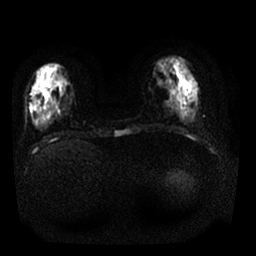
Breast MRI, one axial slice; slice 7 of 25 in the series (ordered by position); diffusion-weighted series; image 2 of 4 stored at this slice position (different b-values; order by instance number); 1.5 T; 256 × 256 image matrix, field of view 330 × 330 mm. Female patient.
Annotated regions visible in this slice (outlined manually by an expert reader):
- tumour on diffusion-weighted imaging: bounding box (x1, y1, x2, y2) in pixels: (179, 92, 189, 102)